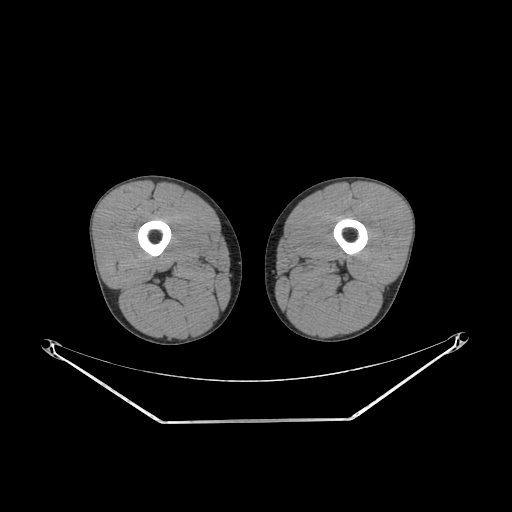
CT of an extremity soft-tissue mass (from a PET/CT study), one axial slice. Position 210 of 267 along the scan axis. Reconstruction kernel SOFT. 140 kVp. Soft-tissue window (W 400 / L 40 HU). 512 × 512 image matrix. Male patient. From the clinical record (not read from this slice): histological type: extraskeletal osteosarcoma; grade: high; site of the primary tumour: left adductur.
Structures marked on this image (expert contour drawn on MRI and transferred to this co-registered scan by the dataset authors):
- gross tumour volume (mass): bounding box [x1, y1, x2, y2] px = [340, 260, 346, 266]